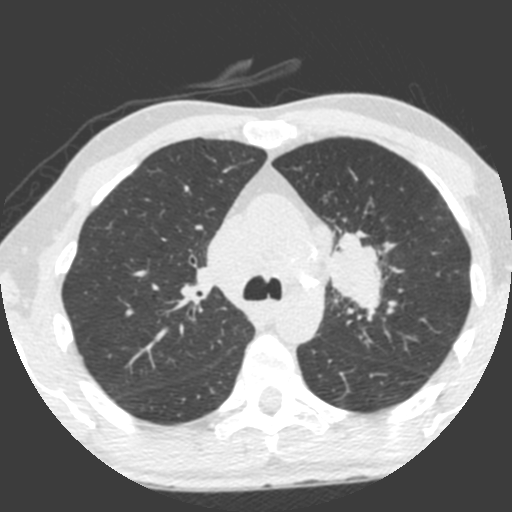
Low-dose screening chest CT, one axial slice. Slice 149 of 212 in the series (ordered by position). Lung window (W 1500 / L -600 HU). 2 mm slice thickness. 512 × 512 image matrix, field of view 315 × 315 mm.
Outlined on this slice (outlined manually by an expert reader):
- lesion 1 (tumor, upper lobe of left lung): bounding box [x1, y1, x2, y2] px = [329, 230, 383, 315]